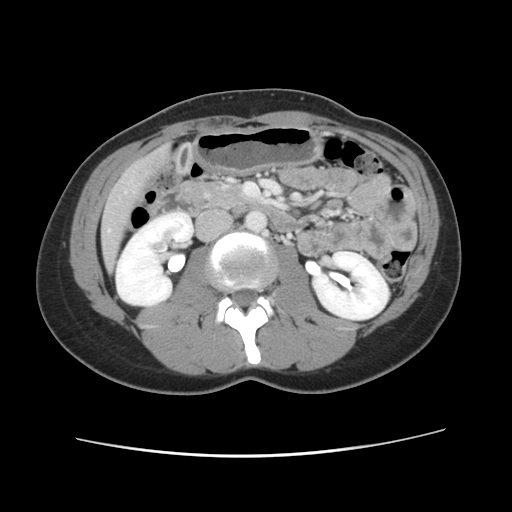
Contrast-enhanced abdominal CT, one axial slice; soft-tissue window (W 400 / L 40 HU); 2.5 mm slice thickness; 512 × 512 image matrix, field of view 339 × 339 mm. Female patient, age 33 years. From the clinical record (not read from this slice): diagnosis: colorectal cancer liver metastases, imaged before liver resection; multiple liver metastases: yes.
Outlined on this slice (expert manual segmentation):
- liver: bounding box [x1, y1, x2, y2] px = [101, 149, 171, 270]
- planned liver remnant (the part of the liver to remain after resection): [102, 244, 116, 270]